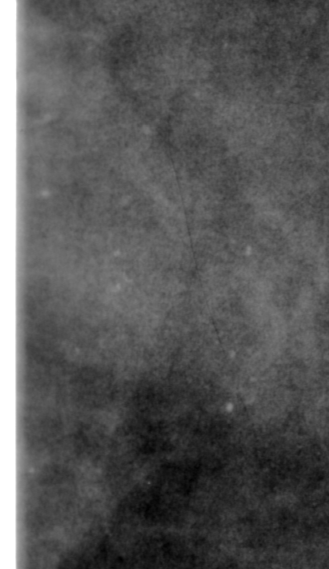
Region of interest cut from a scanned film mammogram (one marked finding); right breast; MLO view; BI-RADS breast density category 4 (scale 1–4).
- Marked abnormality: calcifications, morphology pleomorphic, distribution clustered; BI-RADS assessment category 4; subtlety rating 2 on a 1 (subtle) to 5 (obvious) scale; pathology (as recorded): benign.